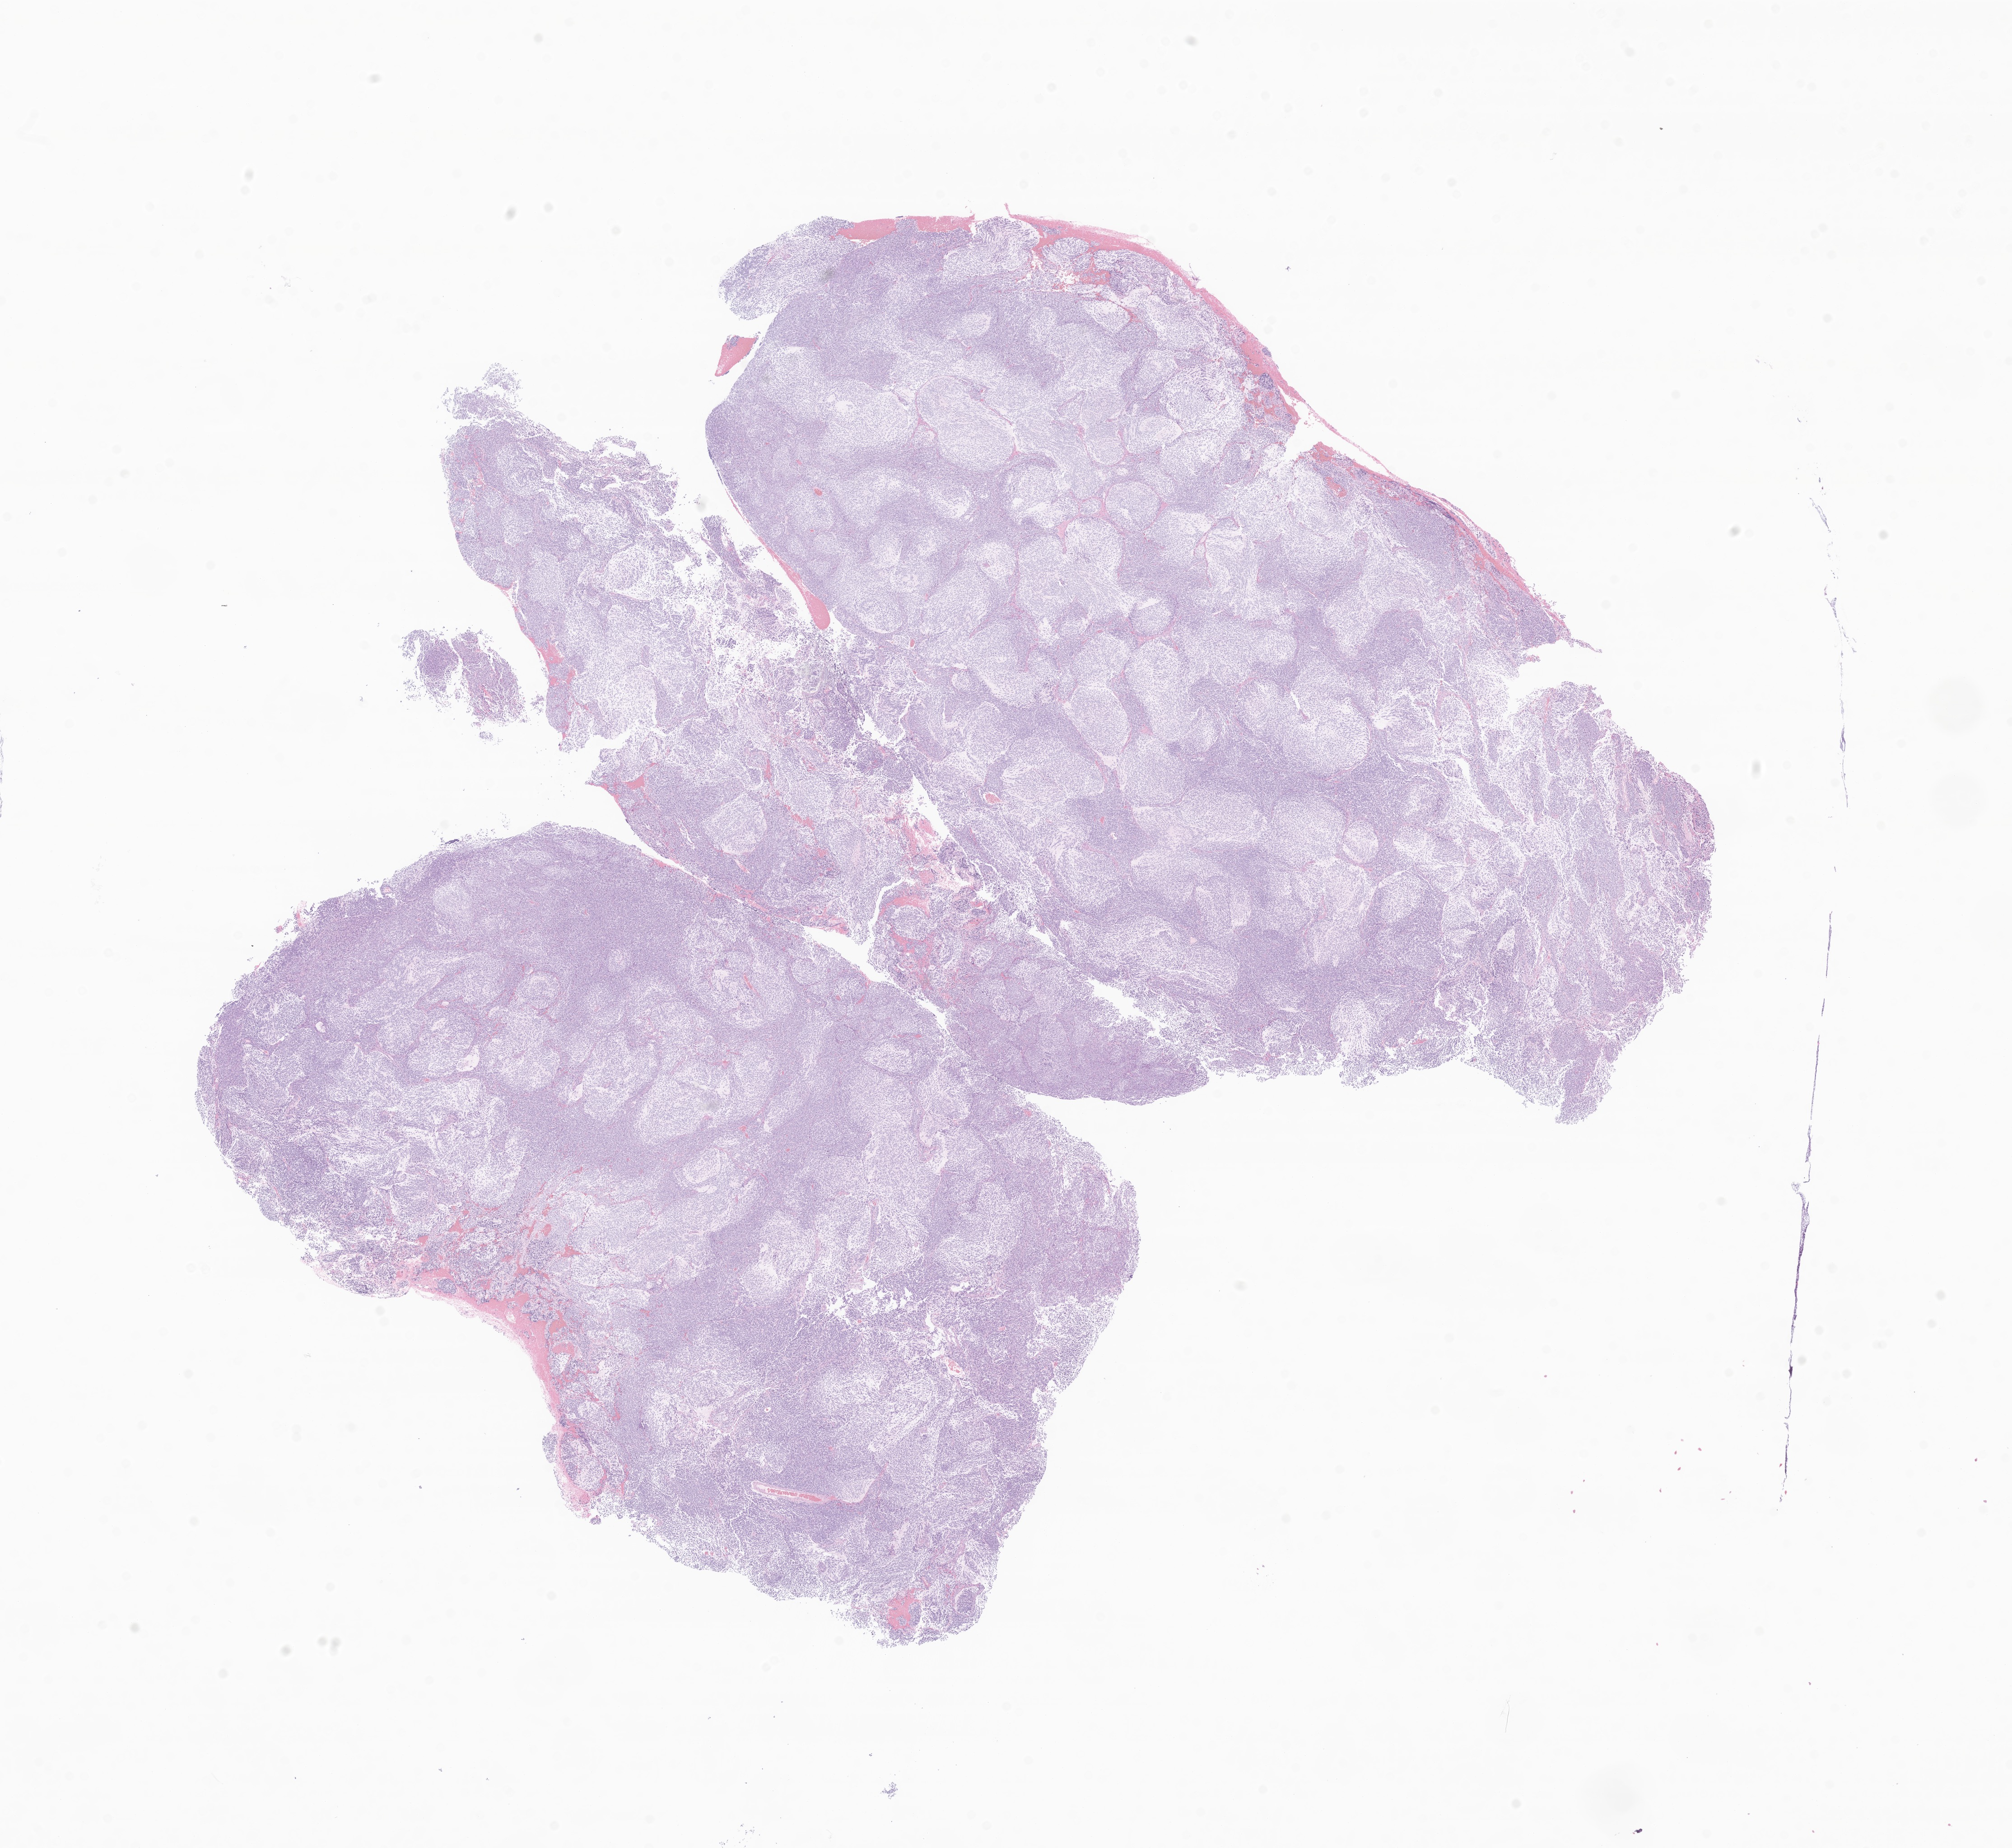
Haematoxylin and eosin whole-slide image of tumor tissue from the cerebellum — low-resolution overview of the scanned area, about 18.8 x 17.3 mm, formalin-fixed, paraffin-embedded (FFPE) tissue. Patient: female, age 119 months.
• diagnosis: Medulloblastoma, NOS